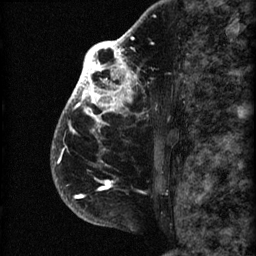
Breast MRI (dynamic contrast-enhanced), one sagittal slice. Position 46 of 60 along the scan axis. 3 images stored at this slice position (order not interpretable as contrast timing). 1.5 T. TE 4.2 ms, TR 22.7 ms. 2 mm slice thickness. 256 × 256 image matrix. Patient: female, 48 years. From the clinical record (not read from this slice): setting: breast cancer imaged before/during neoadjuvant chemotherapy; receptor status: triple-negative.
Annotated regions visible in this slice (semi-automatically segmented with operator editing):
- analysis volume of interest (the breast-tissue region the enhancement analysis was run in; not a lesion): box from (x=50, y=30) to (x=173, y=207) px
- tumour enhancement mask (voxels above the 90 % enhancement threshold inside the analysis volume of interest): (x=53, y=30)–(x=134, y=198)